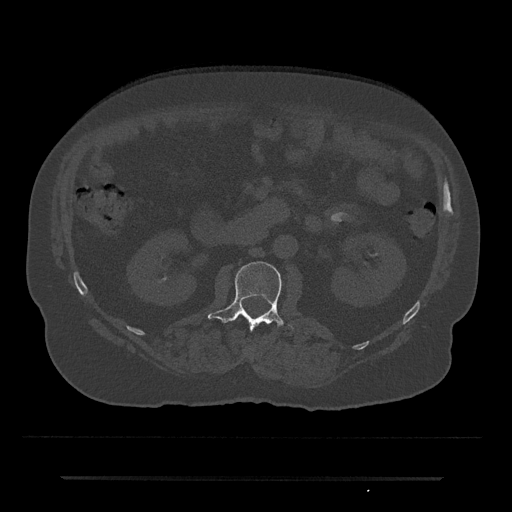
CT including the spine, one axial slice. Slice 17 of 797 in the series (ordered by position). Reconstruction kernel Br40s/3. 120 kVp. Bone window (W 1800 / L 400 HU). 512 × 512 image matrix, field of view 437 × 437 mm. Male patient, age 69 years. From the clinical record (not read from this slice): primary cancer: prostate.
Structures marked on this image (semi-automatically segmented with operator editing):
- L2 vertebra: bounding box [x1, y1, x2, y2] px = [208, 261, 294, 330]